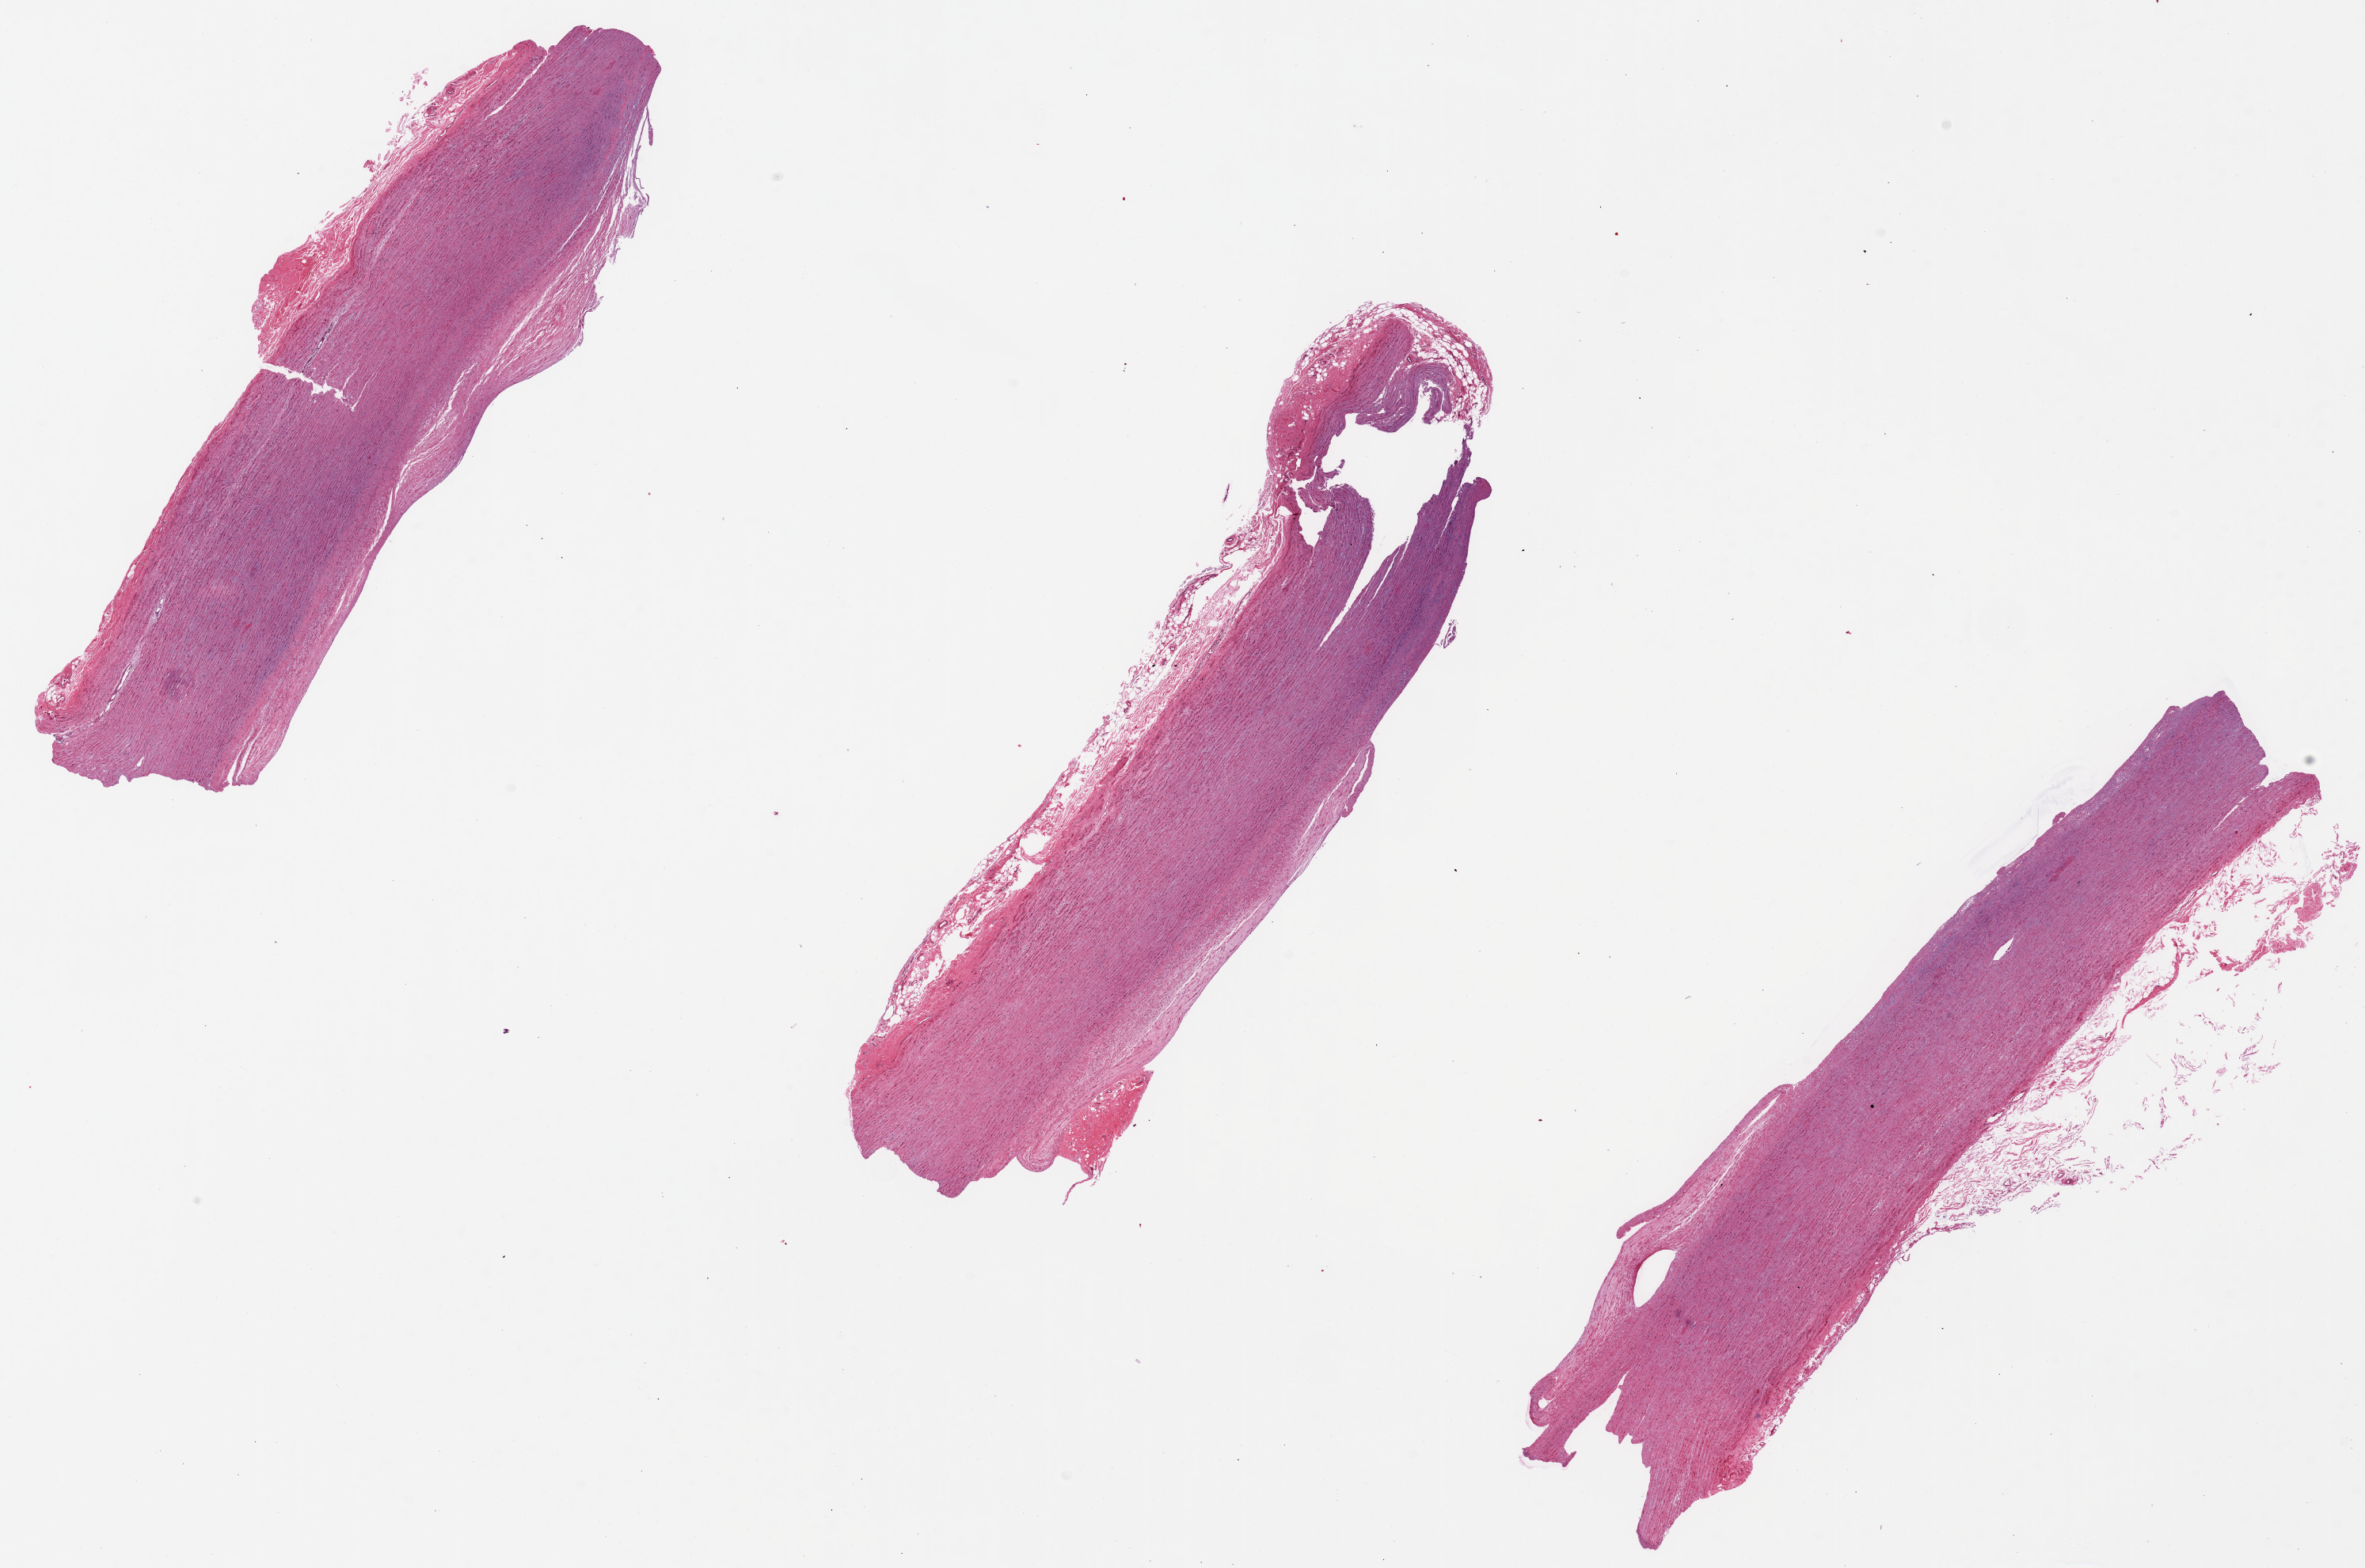
Digitized hematoxylin and eosin (H&E)-stained section, shown as a low-resolution overview of the whole scanned area (about 23.6 x 15.7 mm), PAXgene-fixed, paraffin-embedded tissue, target tissue: aorta, donor tissue sample.
- reviewer comment on this tissue sample: Minimal atherosis